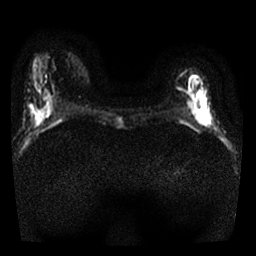
Breast MRI, one axial slice; diffusion-weighted series; image 2 of 4 stored at this slice position (different b-values; order by instance number); 1.5 T; 256 × 256 image matrix, field of view 300 × 300 mm. Female patient.
Structures marked on this image (manually delineated by an expert):
- tumour on diffusion-weighted imaging: box from (x=176, y=74) to (x=212, y=127) px